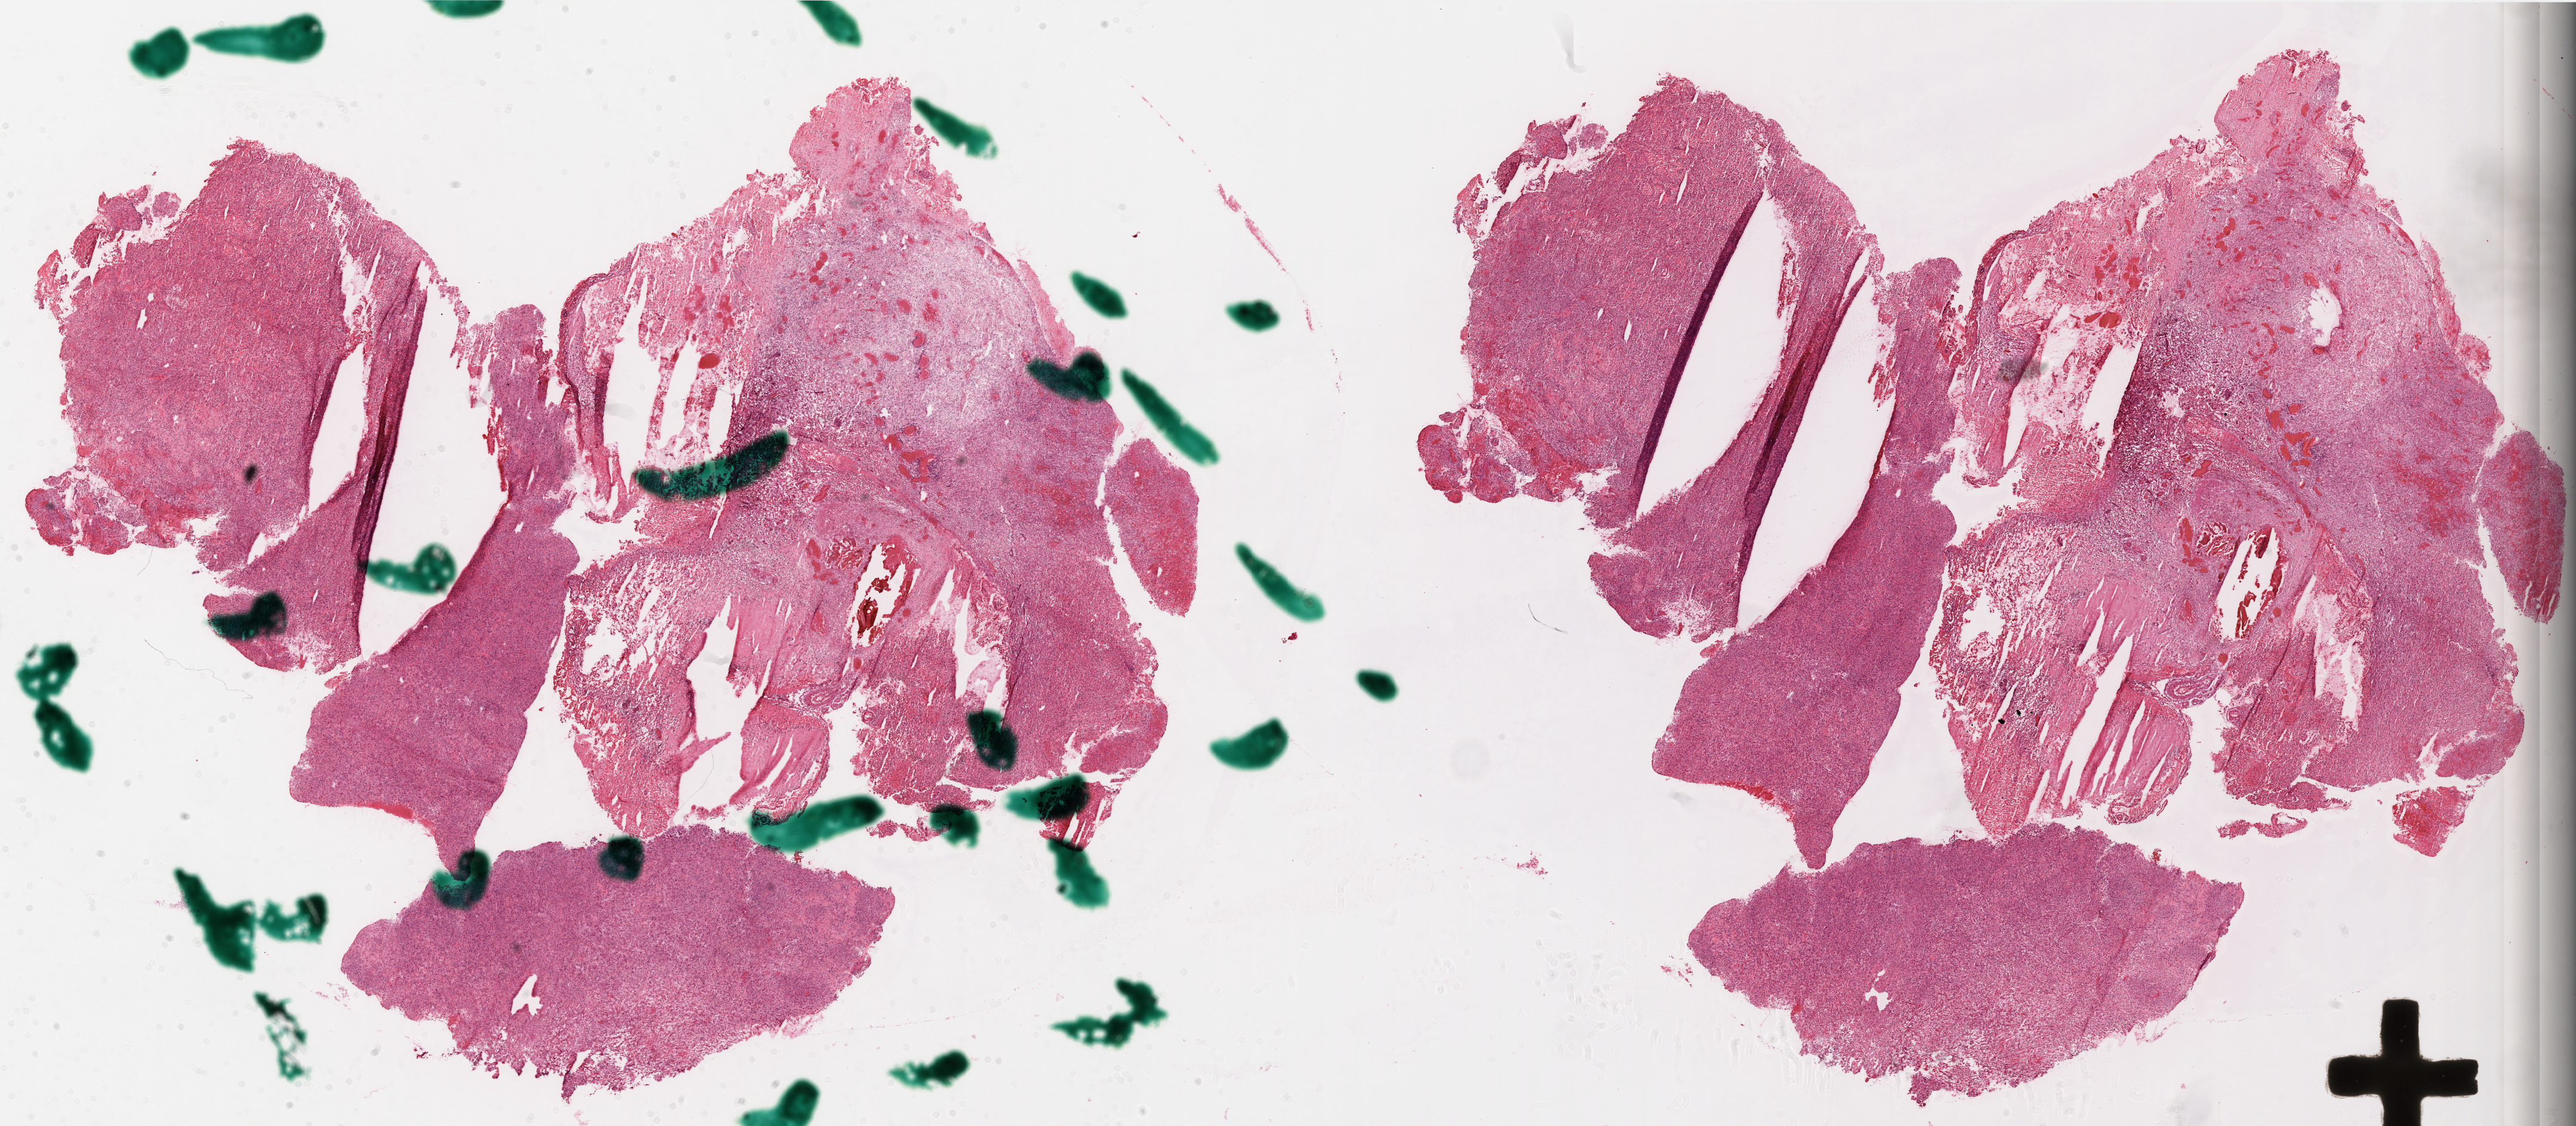
Whole-slide histology image, Hematoxylin and eosin (H&E) stained — whole scanned area (about 34.7 x 15.2 mm) shown as a low-resolution overview, frozen section from the top of the tissue portion, brain, primary tumour sample. Patient: male, age at initial diagnosis 47 years. Composition of this section per pathologist review: tumour cells 80%, tumour nuclei 100%, normal cells 0%, stromal cells 0%, necrosis 20%.
Diagnosis: Glioblastoma.